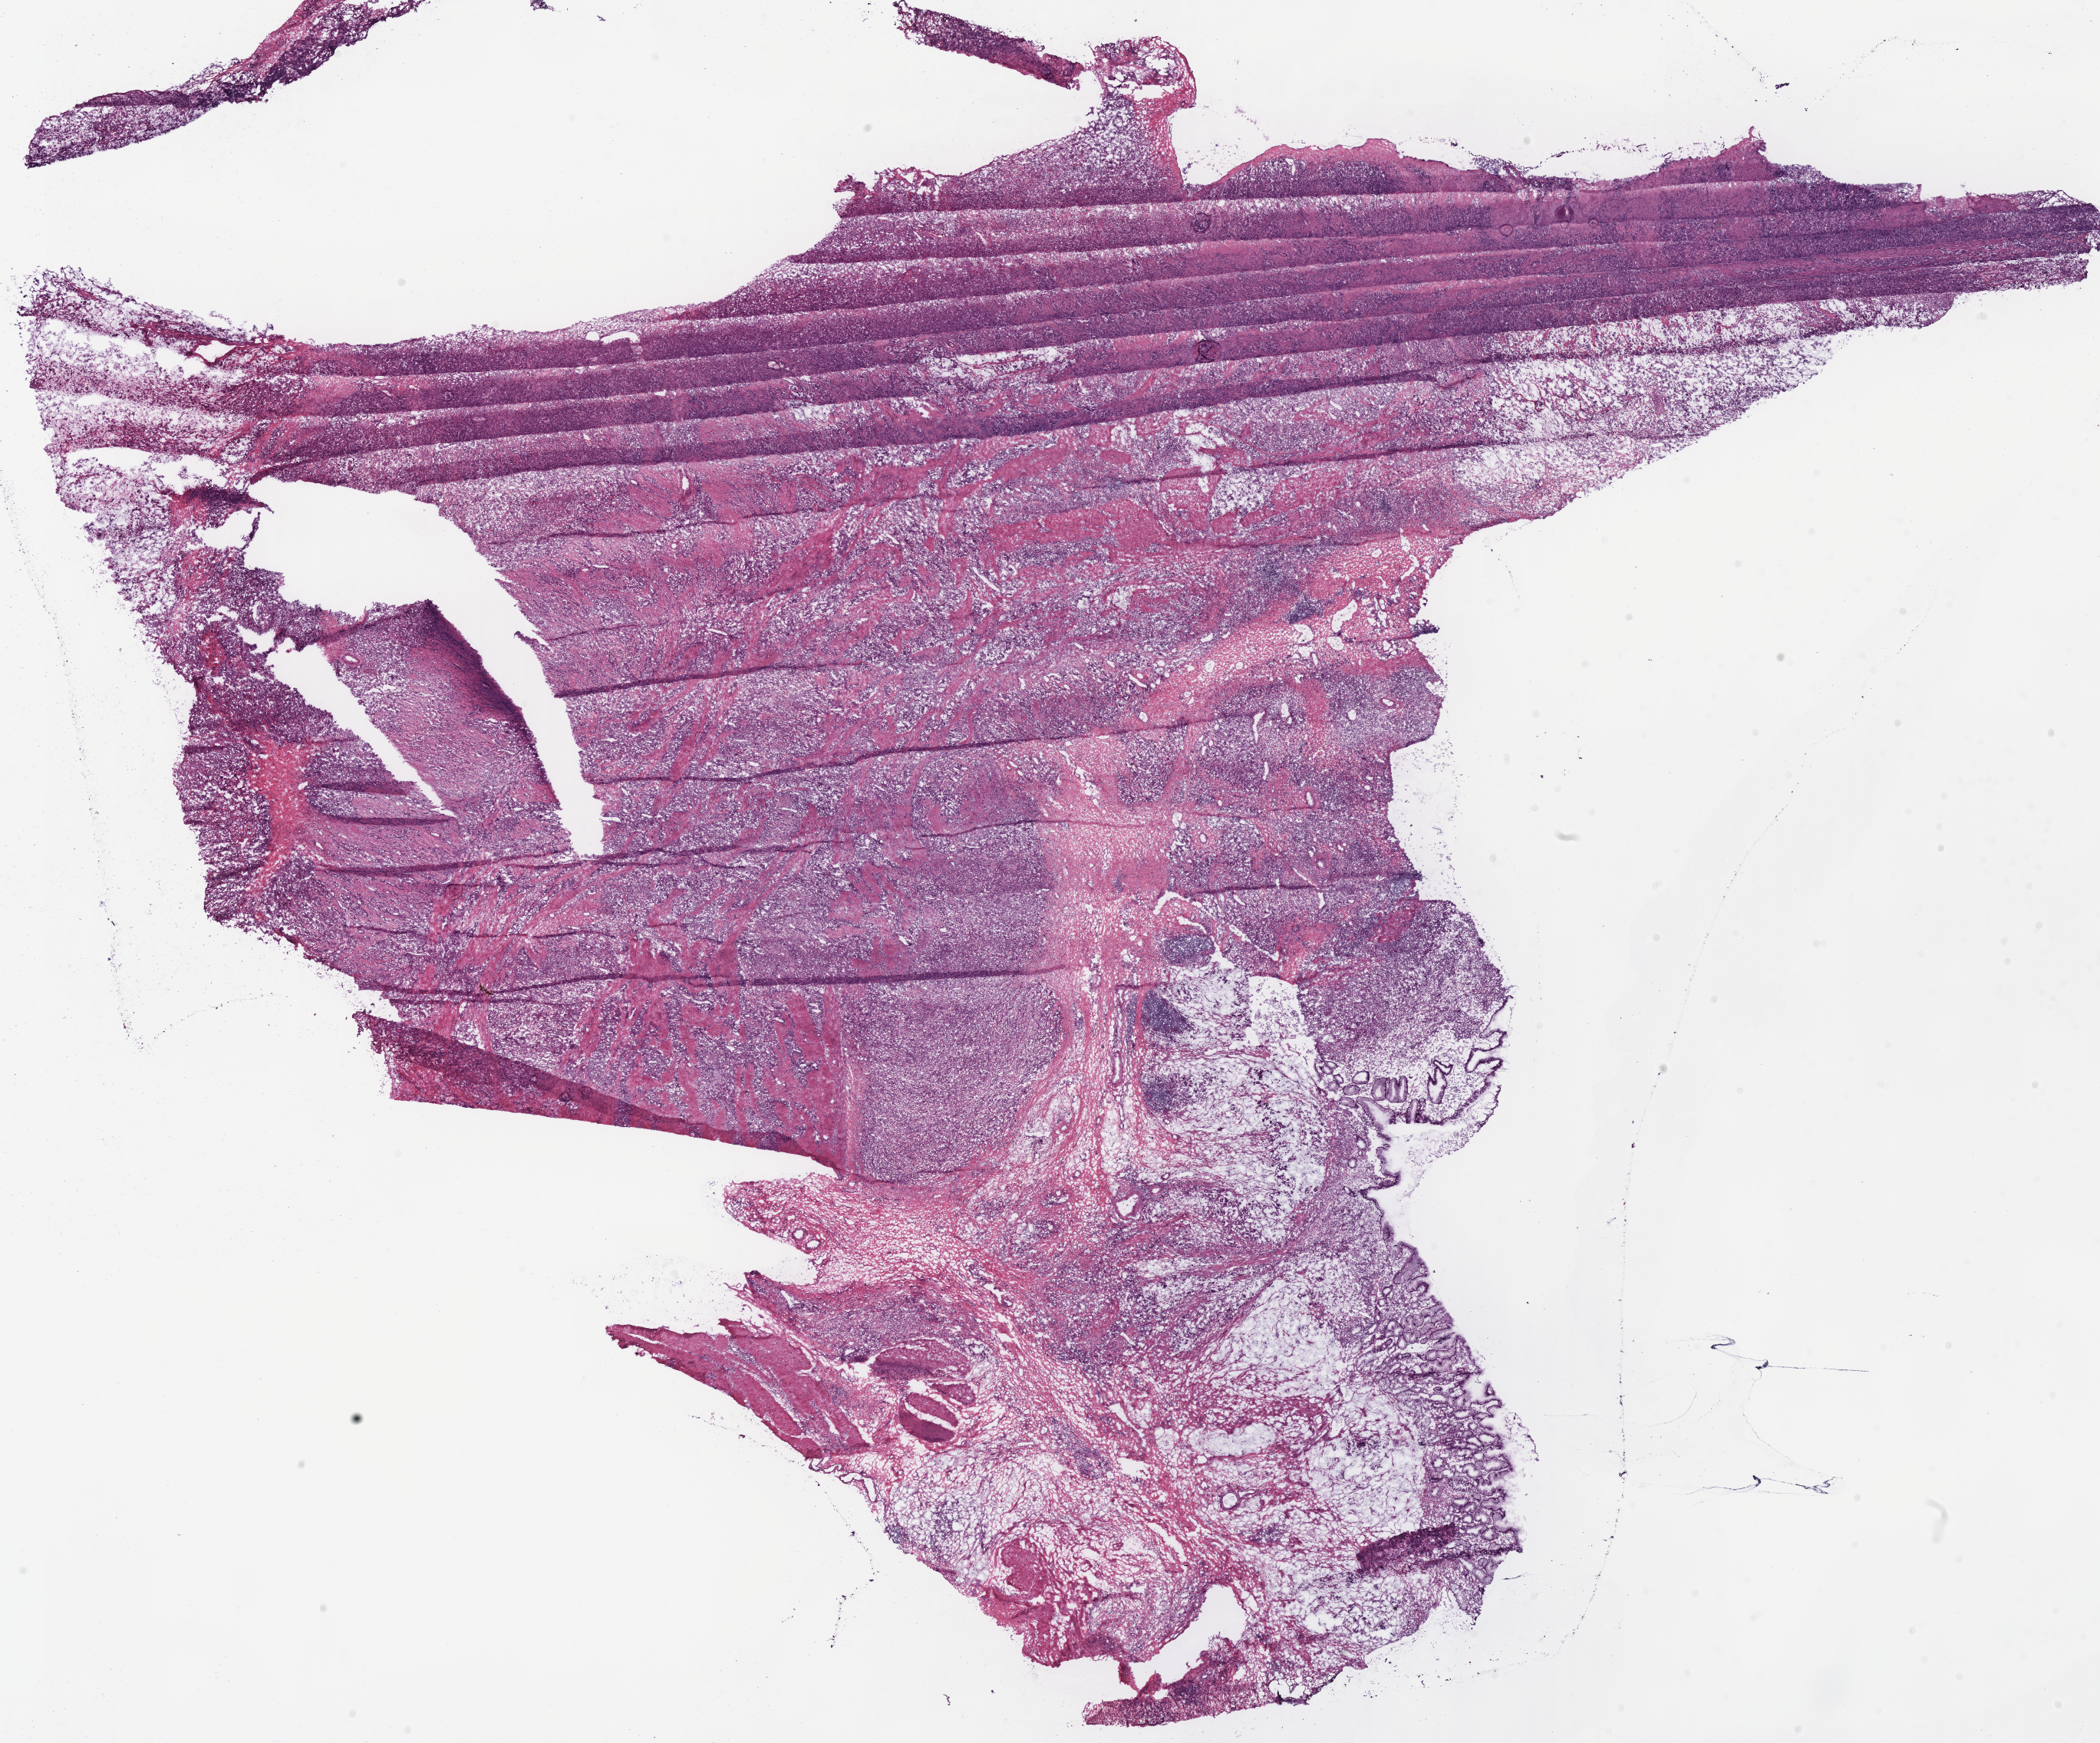
Digitized Hematoxylin and eosin (H&E) stained tissue section (whole slide) — a low-resolution overview of the entire scanned area, about 21.6 x 17.9 mm (acquisition: 40x scan); frozen section; primary tumour sample from the stomach. Male patient; age at initial diagnosis 64 years. Histologic grade: G3 (poorly differentiated). Pathologist review of this section (percent, as recorded): tumour cells 72%, tumour nuclei 80%, normal cells 8%, stromal cells 15%, necrosis 5%.
Pathologic diagnosis: Adenocarcinoma, NOS (cardia, NOS). AJCC pathologic stage: IIIB.